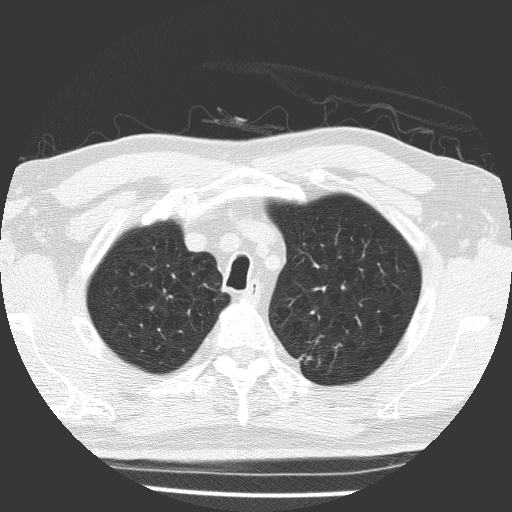
Chest CT (low-dose screening protocol), one axial image; first (baseline) screen; lung window (W 1500 / L -600 HU); slice 32 of 169 in the series; 512 × 512 image matrix, field of view 323 × 323 mm. Male, age 64 years at enrolment. Former smoker at enrolment.
Lesion marked by an expert reader, bounding box <282,341,328,381> (left, top, right, bottom; pixels). The exam's reader record, not a measurement of the box and not confirmed to be the same lesion: non-calcified nodule or mass ≥4 mm, left upper lobe, 9 × 7 mm, spiculated (stellate) margins, soft tissue attenuation. Official screen result: positive, change unspecified: nodule(s) >= 4 mm or enlarging nodule(s), mass(es), or other non-specific abnormalities suspicious for lung cancer. Participant outcome: lung cancer diagnosed 70 days after this screen — adenocarcinoma, NOS, left upper lobe, poorly differentiated (G3), stage IIA (AJCC 6th edition), 9 mm at pathology.